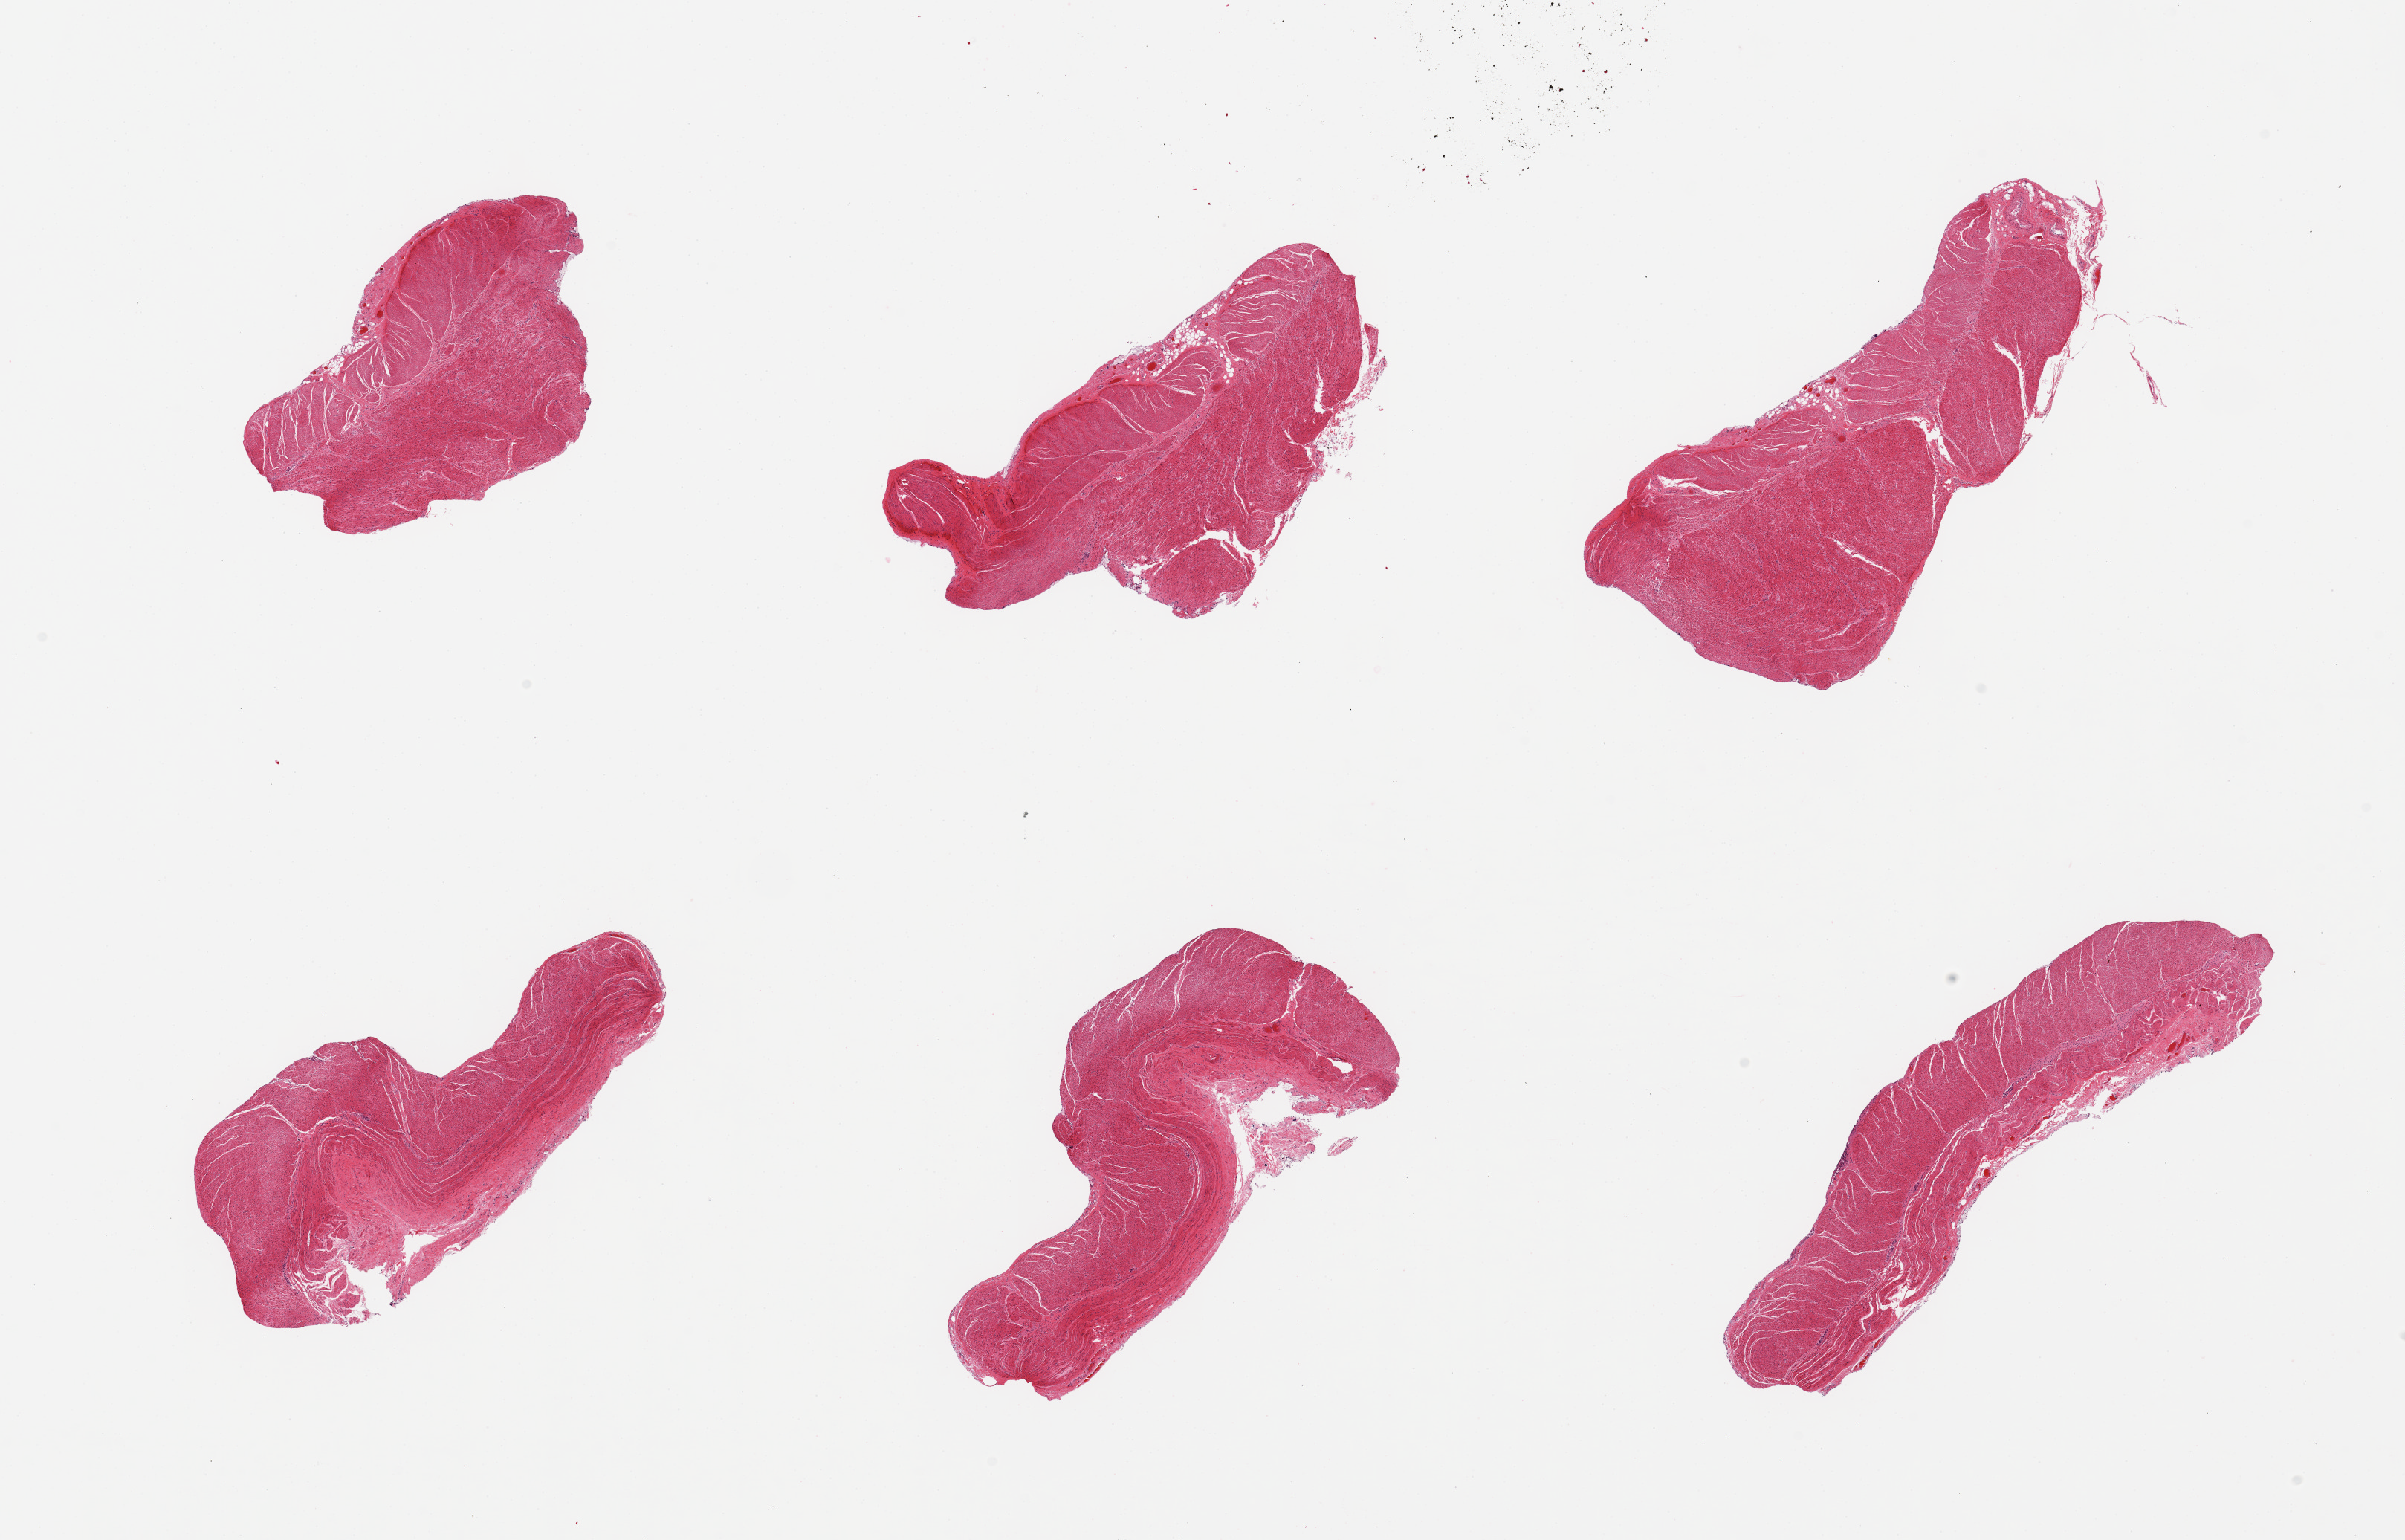
Digitized hematoxylin and eosin (H&E)-stained section — whole scanned area (about 25.6 x 16.4 mm, slide scanned at 20x) shown as a low-resolution overview; PAXgene-fixed, paraffin-embedded tissue; section of sigmoid colon (target tissue); tissue donor sample. Donor: male.
Pathologist's review note for this sample: 6 pieces; well trimmed.